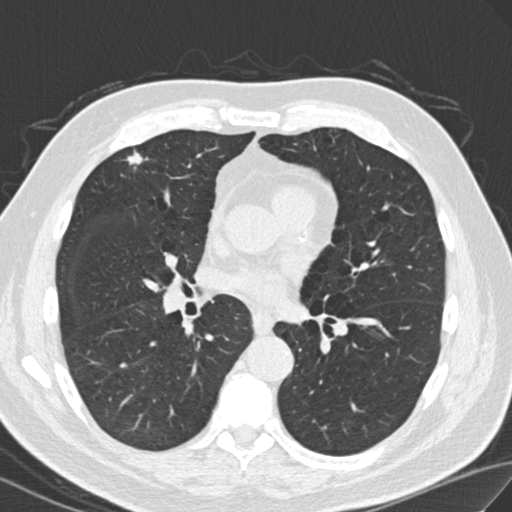
Chest CT (low-dose screening protocol), one axial image, second screening round (one year after baseline), lung window (W 1500 / L -600 HU), 2 mm slice thickness, slice 89 of 171 in the series. Male participant, aged 69 years at enrolment. Current smoker at enrolment.
Expert-annotated lung lesion, bounding box (x1, y1, x2, y2) in pixels: (110, 140, 160, 184). The screening reader recorded 3 non-calcified nodules or masses ≥4 mm on this exam; which of them this box marks is not recorded. Later outcome: lung cancer diagnosed 183 days after this screen — adenocarcinoma, NOS, right upper lobe, moderately differentiated (G2), stage IIA (AJCC 6th edition), 20 mm at pathology.